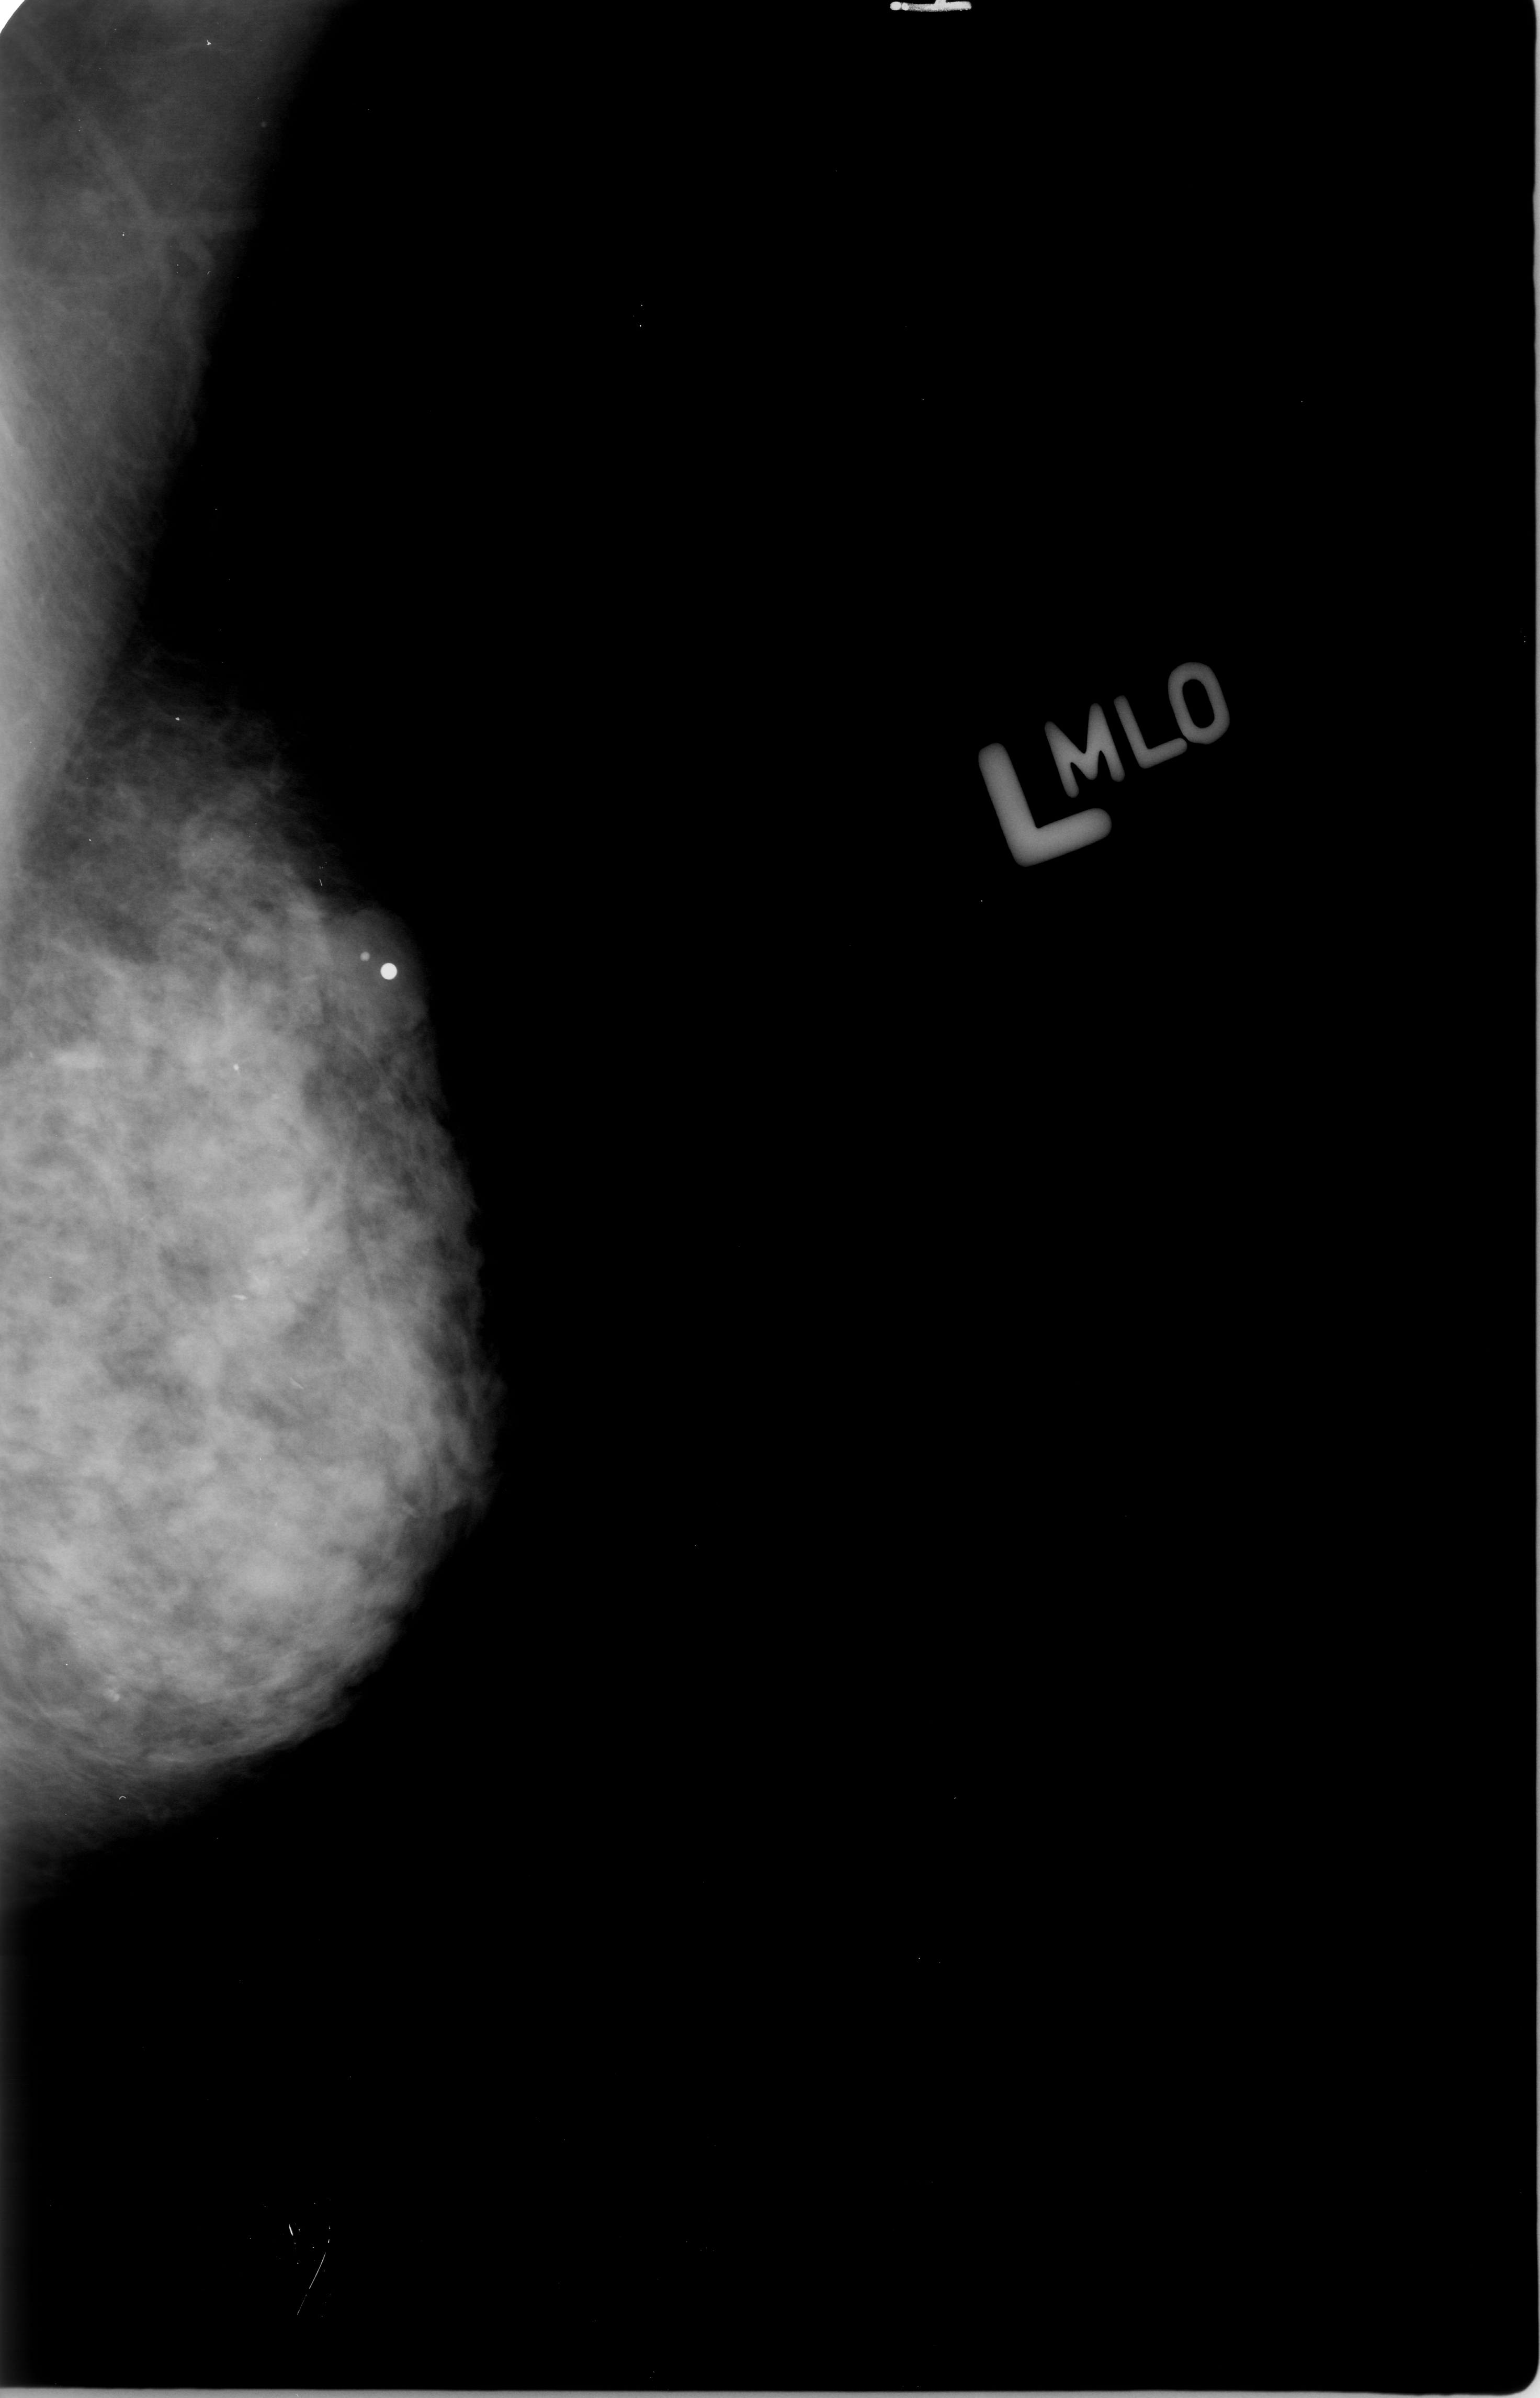
Scanned film-screen mammogram. Left breast. Mediolateral oblique (MLO) view. Breast composition: heterogeneously dense (BI-RADS density category 3 of 4). 1540 × 2398 image matrix.
Marked abnormalities (boxes around the expert regions of interest):
- calcifications, morphology pleomorphic, distribution clustered; BI-RADS assessment category 3; subtlety rating 2 on a 1 (subtle) to 5 (obvious) scale; pathology result (as recorded, not read from the image): malignant: box from (x=242, y=1217) to (x=336, y=1307) px